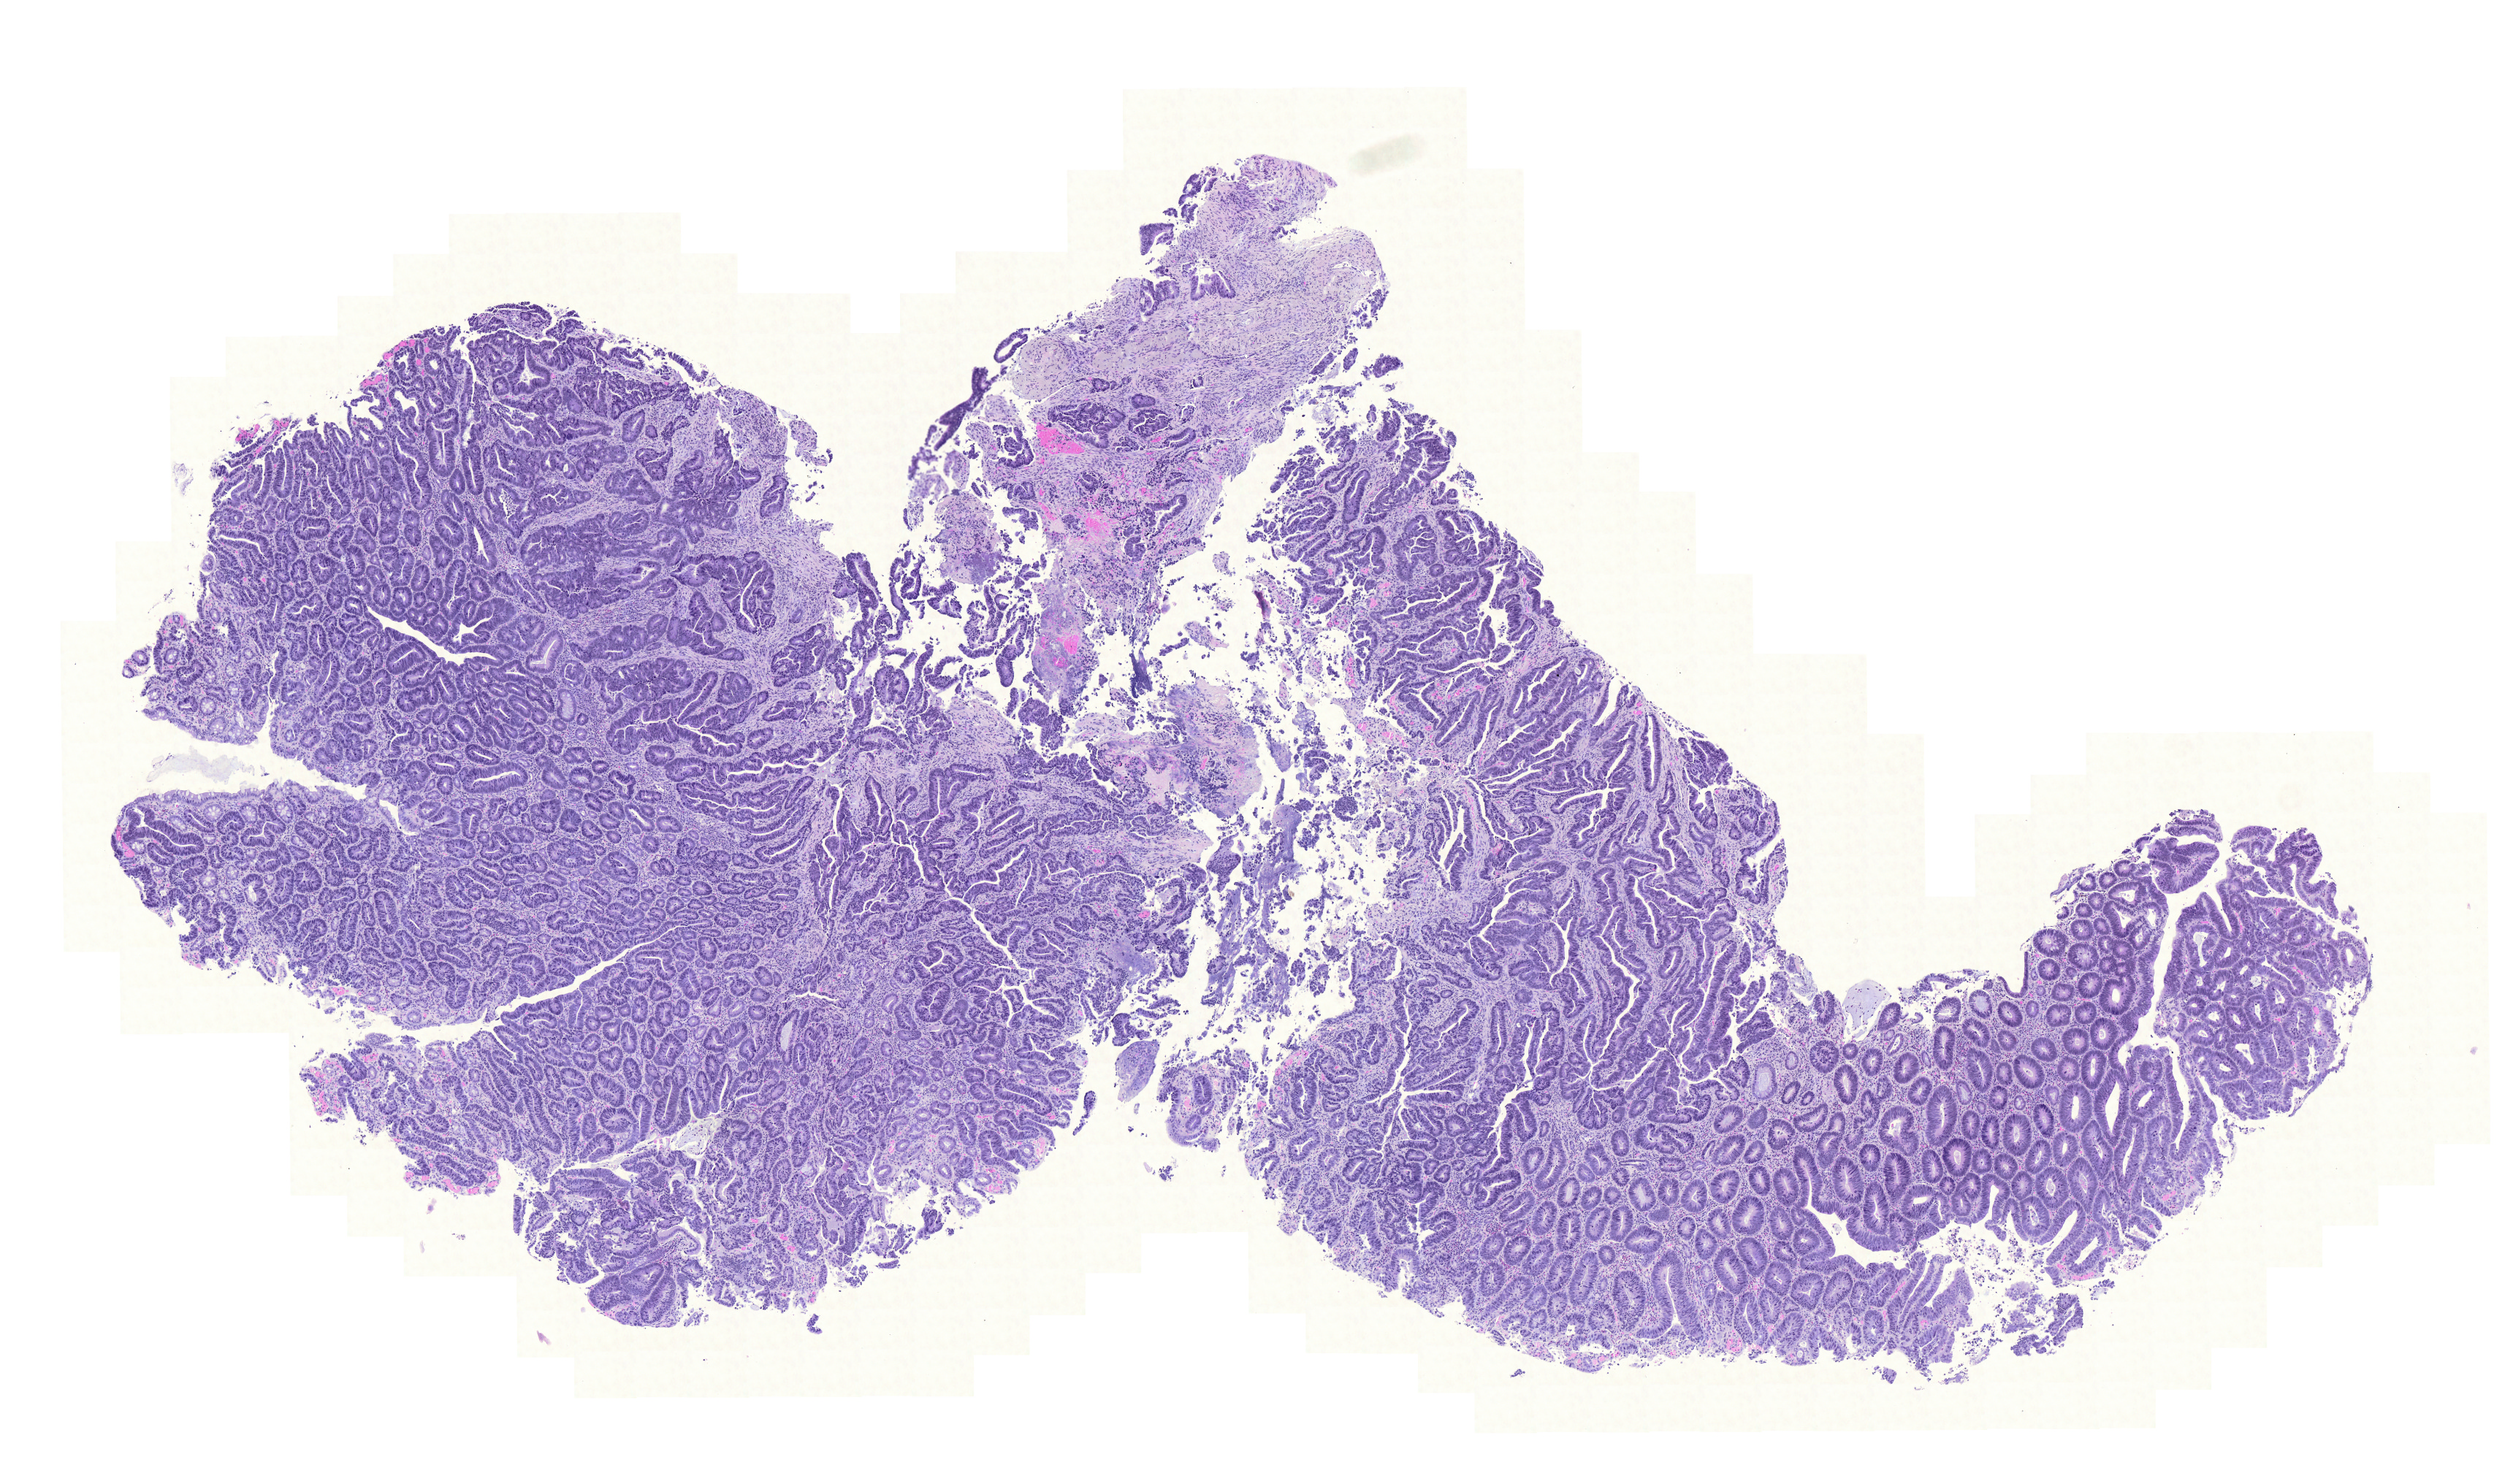
Whole-slide histology image, H&E-stained, low-resolution overview of the scanned area, about 12.8 x 7.6 mm; FFPE section; sample: primary tumour, colon. Male patient; age at initial diagnosis 75 years.
Diagnosis: Adenocarcinoma, NOS (ascending colon). AJCC pathologic stage: IIIA (6th edition). Lymph nodes positive (case pathology): 3 of 31 examined. TNM: T2 N1 M0.